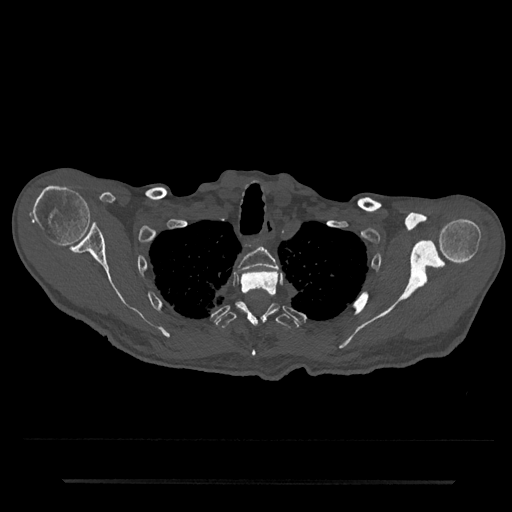
CT including the spine, one axial slice. Slice 651 of 797 in the series (ordered by position). Reconstruction kernel Br40s/3. 120 kVp. Bone window (W 1800 / L 400 HU). 0.5 mm slice thickness. 512 × 512 image matrix, field of view 427 × 427 mm. Patient: male, 74 years. From the clinical record (not read from this slice): primary cancer: prostate.
Outlined on this slice (semi-automatic segmentation, software-assisted and operator-edited):
- T2 vertebra: bounding box [x1, y1, x2, y2] px = [237, 248, 277, 272]
- T3 vertebra: [240, 271, 278, 355]
- T4 vertebra: [216, 301, 300, 329]